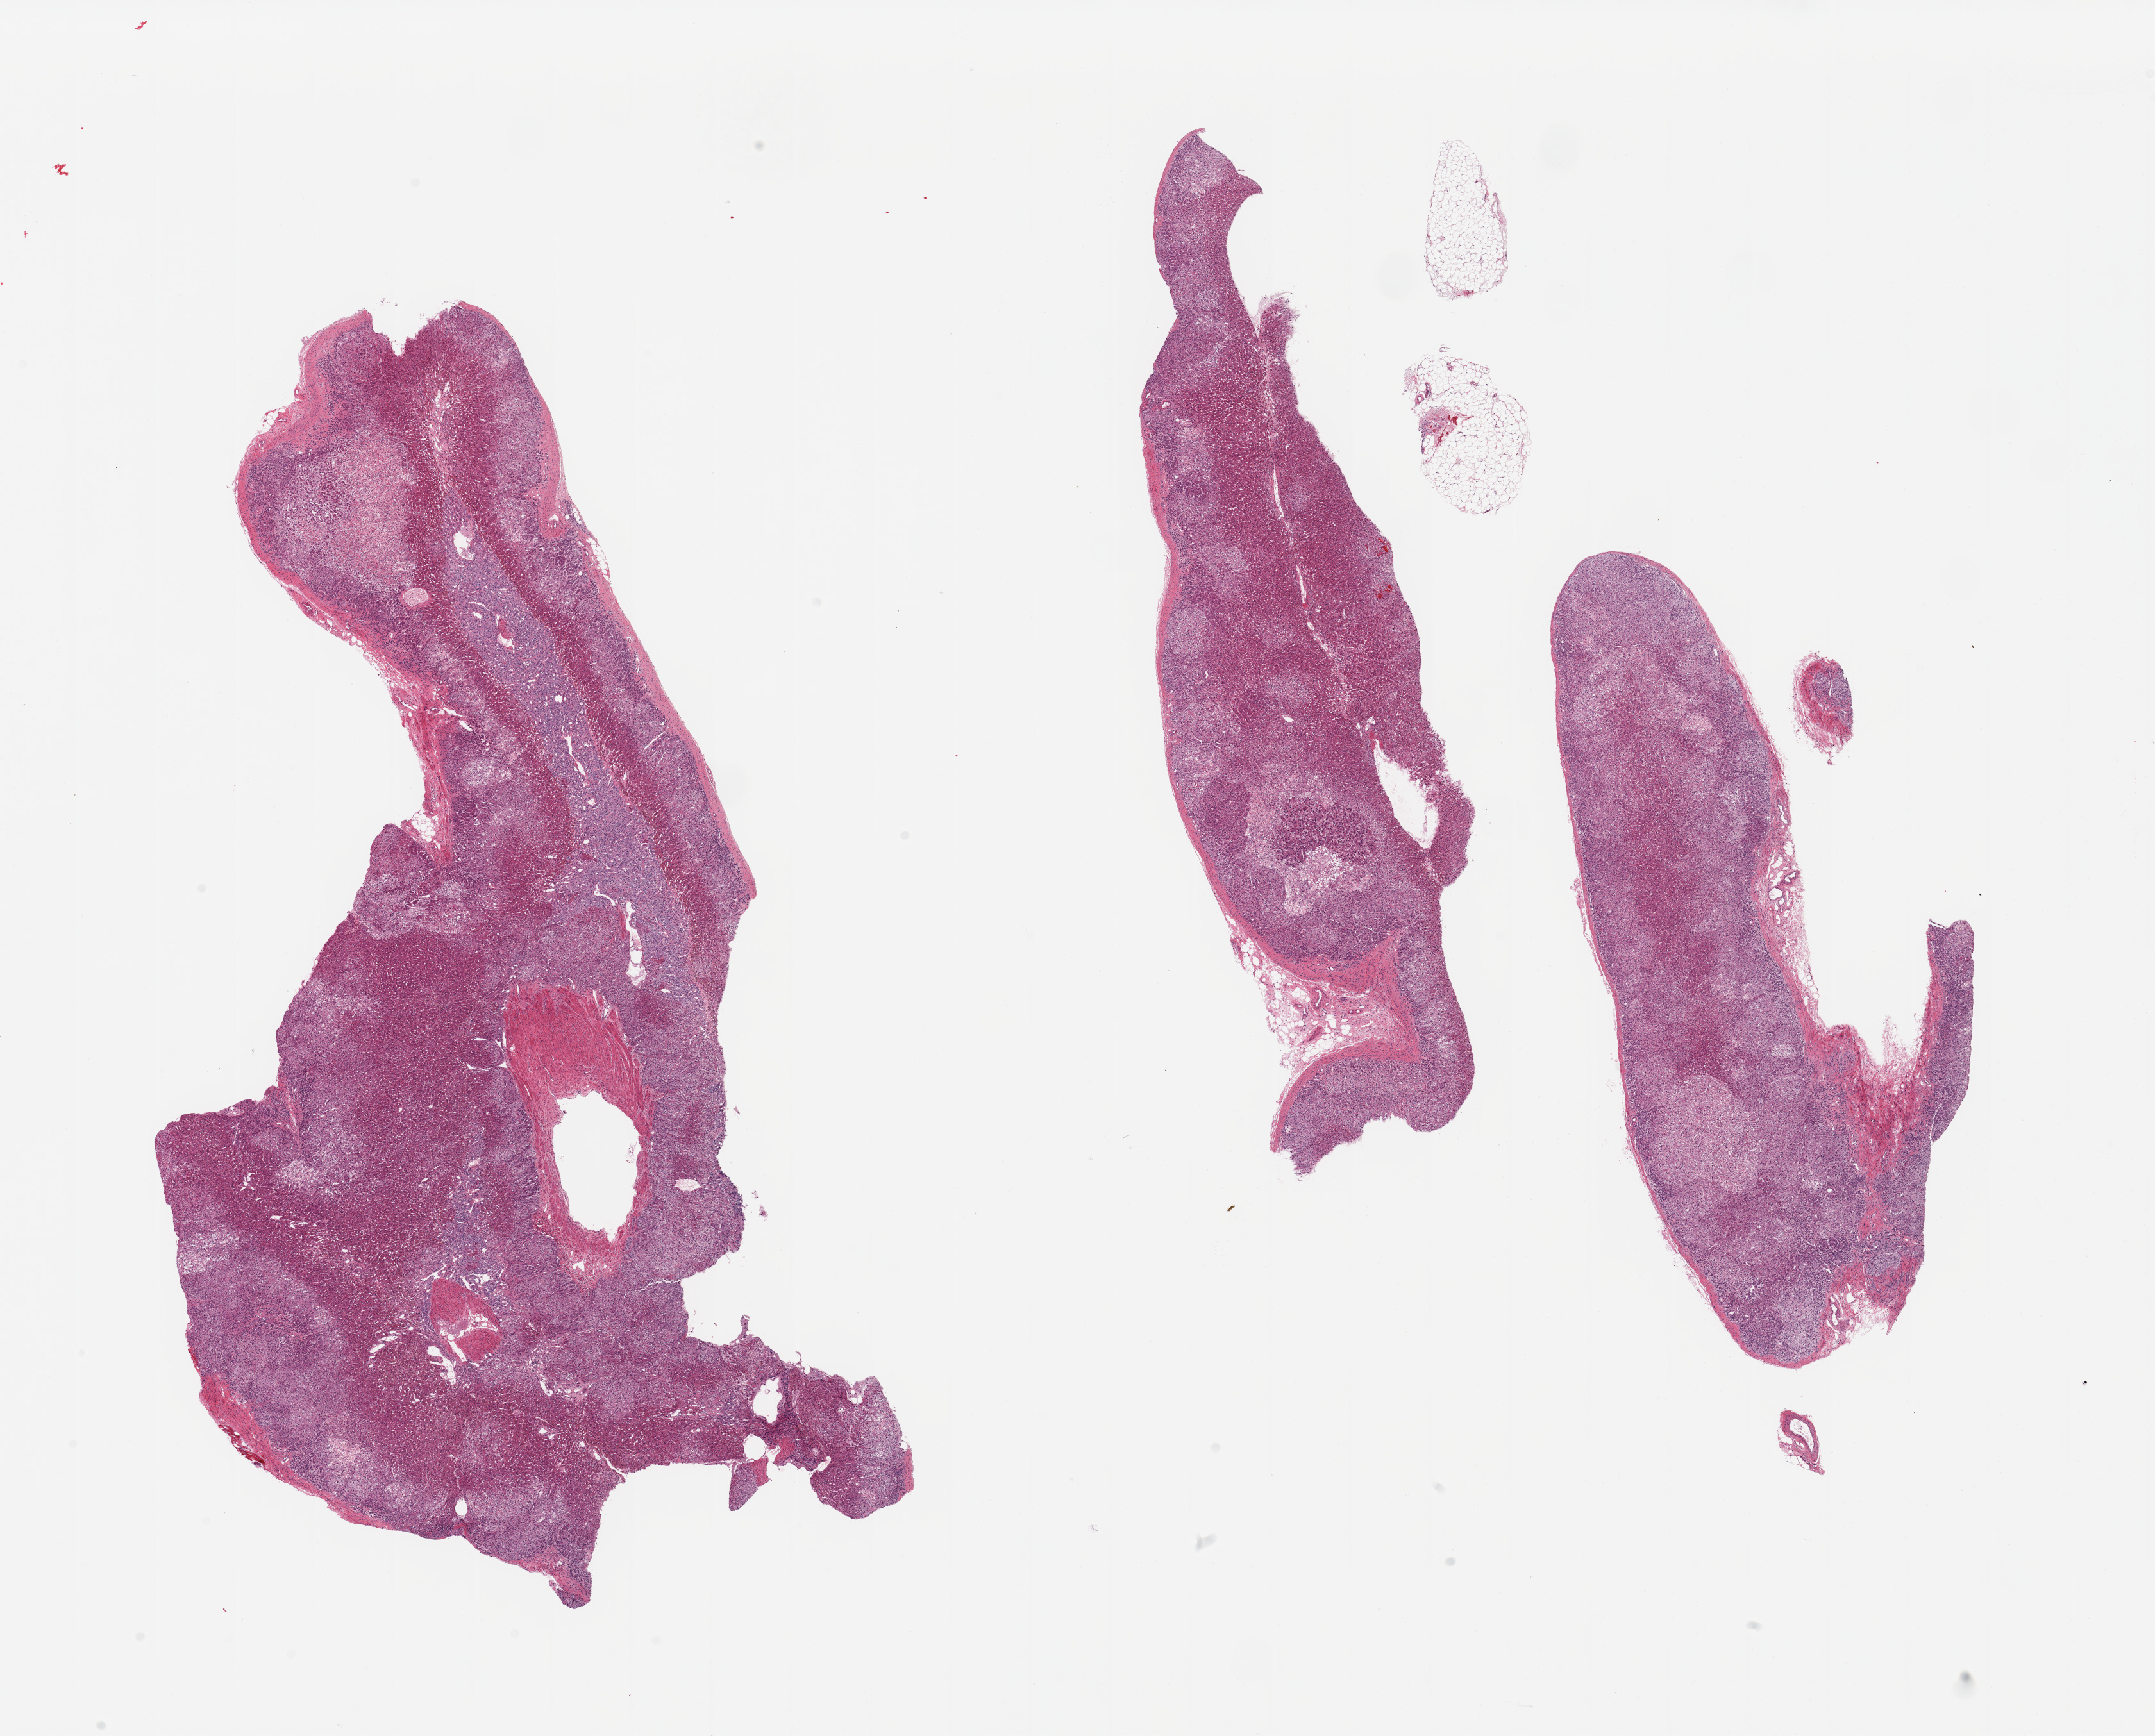
Whole-slide image, H&E stain, brightfield, low-resolution overview of the scanned area, about 26.6 x 21.4 mm. PAXgene-fixed paraffin-embedded (PFPE) section. Target tissue: adrenal gland. Tissue donor sample. Female donor.
- pathologist's review note for this sample: 3 pieces, well preserved cortex and medulla--good specimen